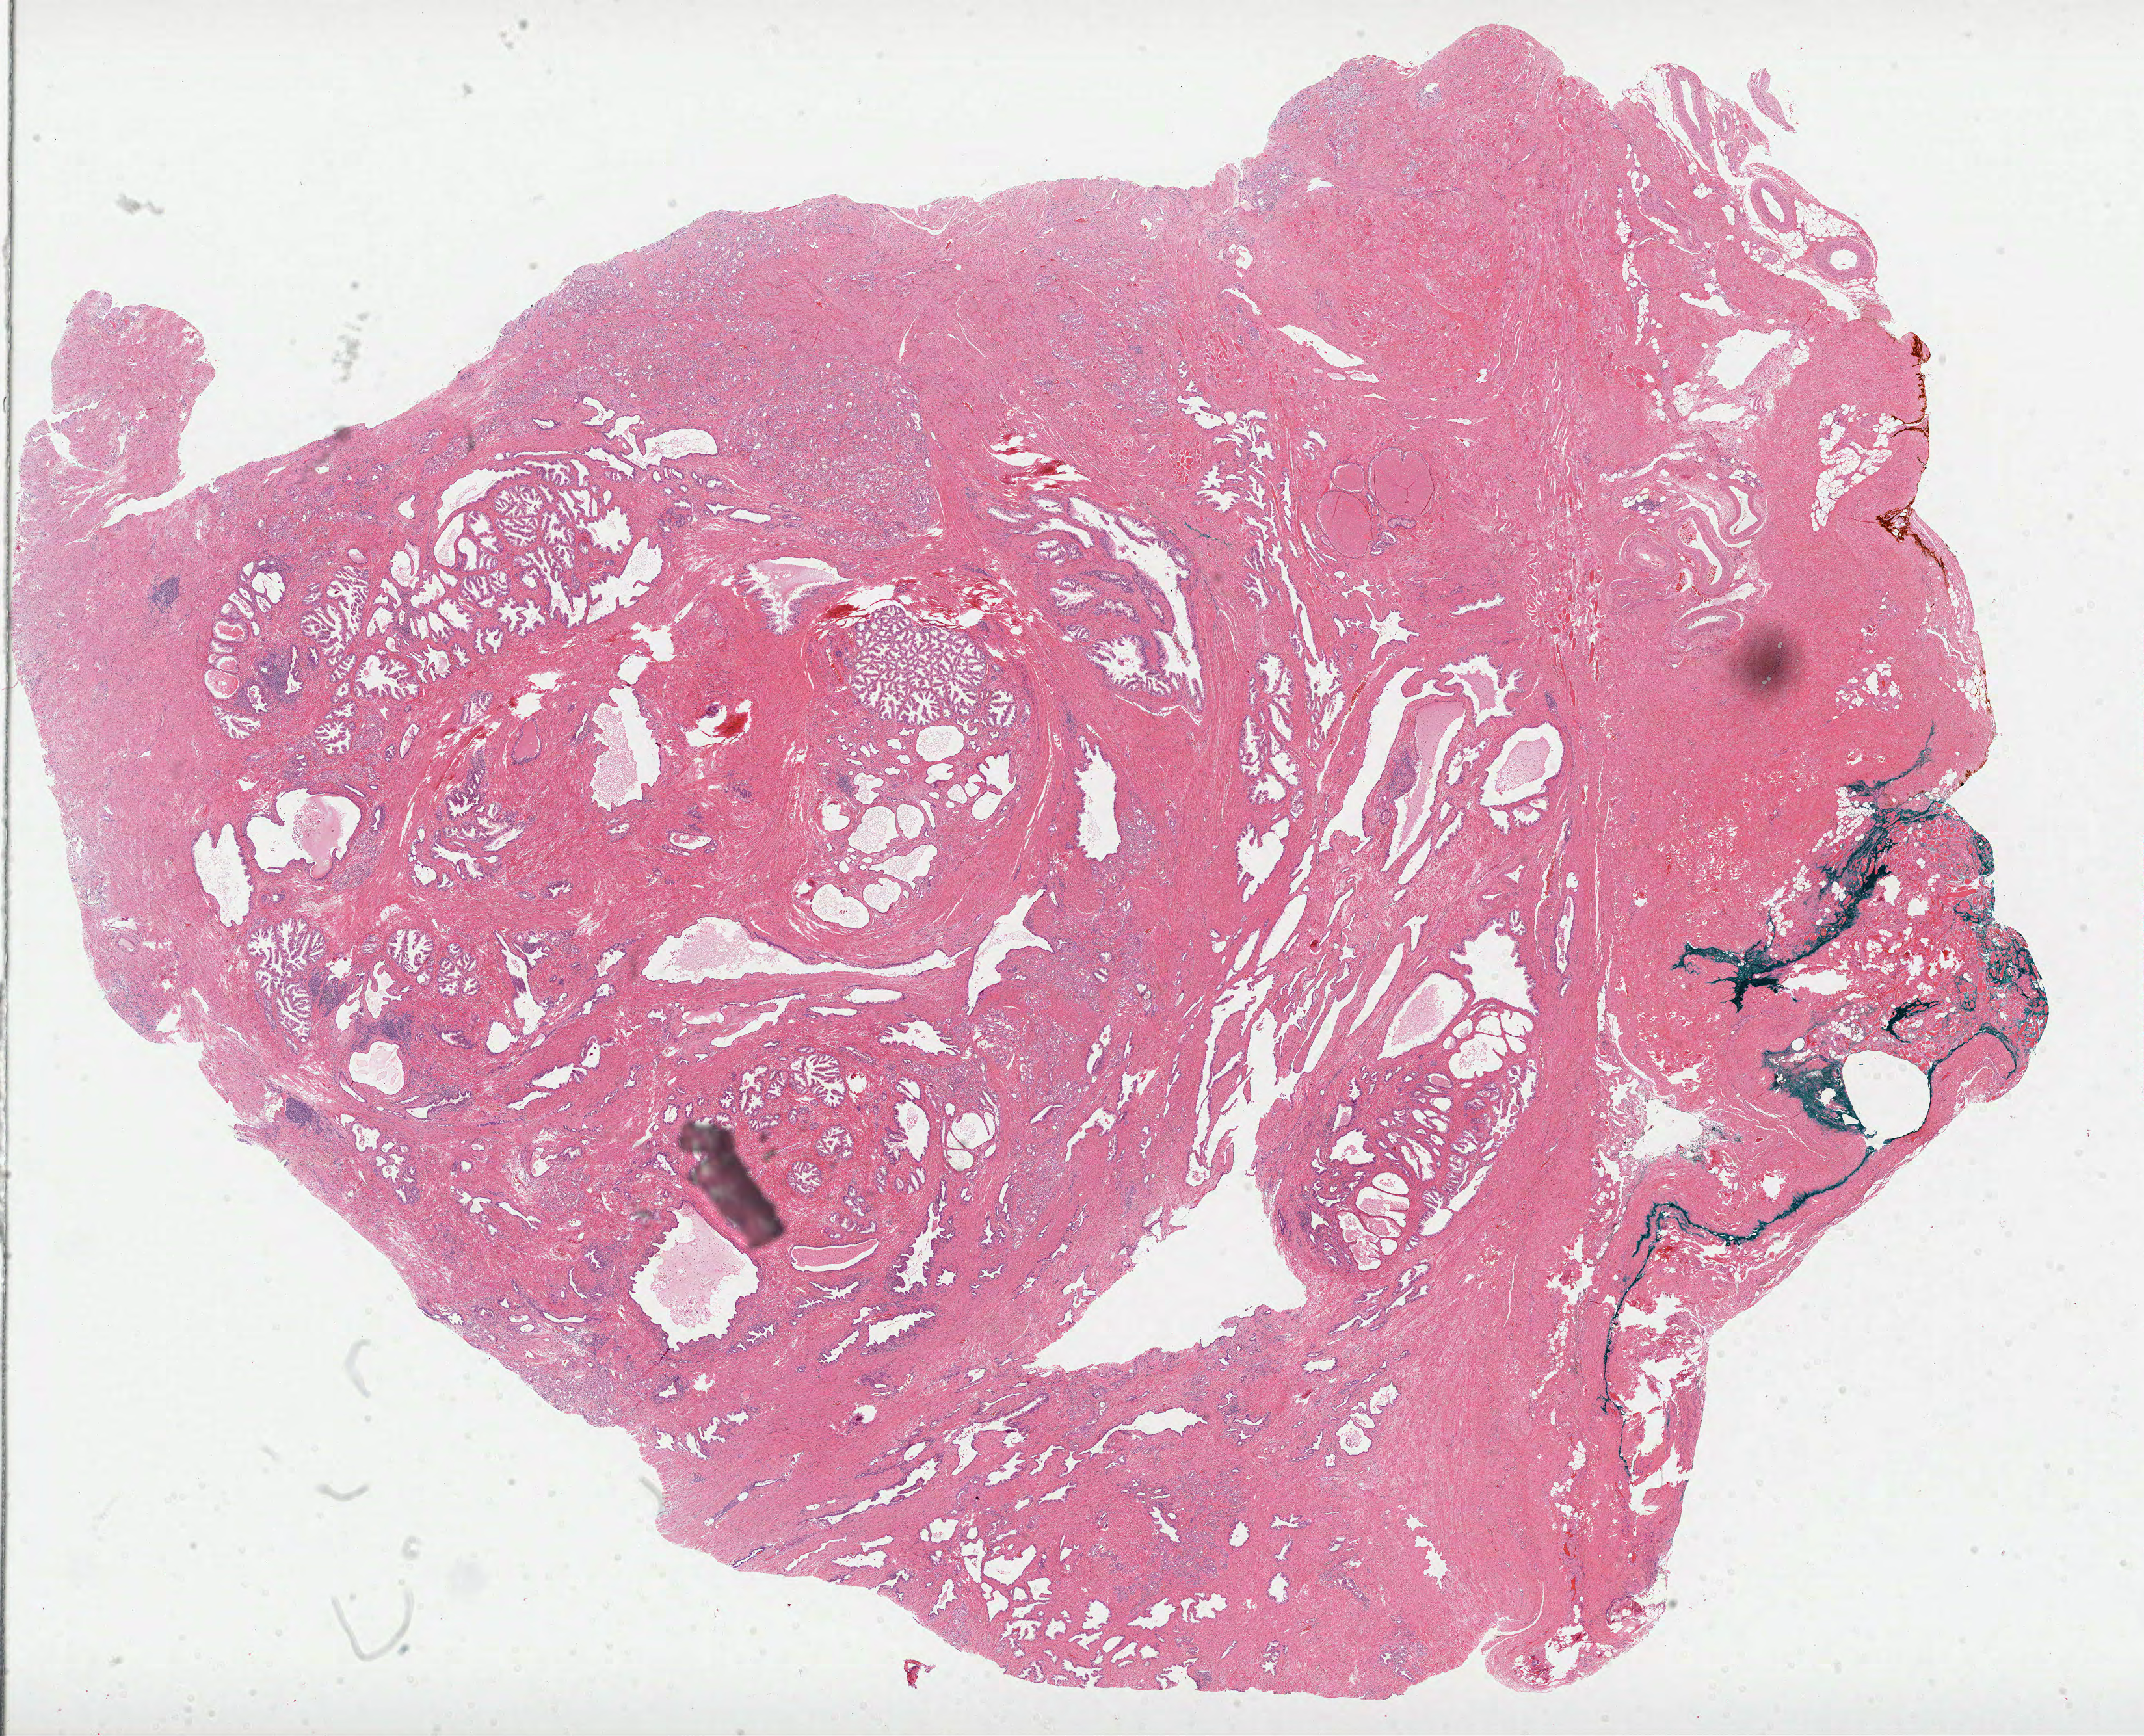
Hematoxylin and eosin (H&E) stained whole-slide image, shown as a low-resolution overview of the whole scanned area (about 26.6 x 21.5 mm), formalin-fixed paraffin-embedded (FFPE) diagnostic section, prostate, primary tumour sample. Male patient; age at initial diagnosis 66 years. Gleason score: 7 (4+3).
* diagnosis: Acinar cell carcinoma (prostate gland)